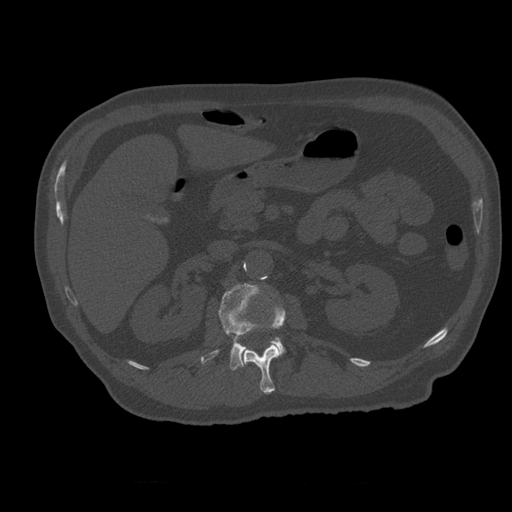
CT including the spine, one axial slice. Slice 227 of 399 in the series (ordered by position). Reconstruction kernel STANDARD. 120 kVp. Bone window (W 1800 / L 400 HU). 1.25 mm slice thickness. 512 × 512 image matrix, field of view 407 × 407 mm. Patient age 73 years. Case-level facts recorded for this patient, not image findings: primary cancer: prostate.
Structures marked on this image (semi-automatic segmentation, software-assisted and operator-edited):
- L1 vertebra: bounding box <241,306,285,394> (left, top, right, bottom; pixels)
- L2 vertebra: <201,284,285,371>